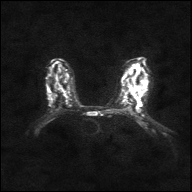
Breast MRI, one axial slice. Slice 20 of 36 in the series (ordered by position). Diffusion-weighted series; image 2 of 4 stored at this slice position (different b-values; order by instance number). 1.5 T. 192 × 192 image matrix, field of view 360 × 360 mm. Female patient.
Annotated regions visible in this slice (expert manual segmentation):
- tumour on diffusion-weighted imaging: bounding box <50,101,53,106> (left, top, right, bottom; pixels)